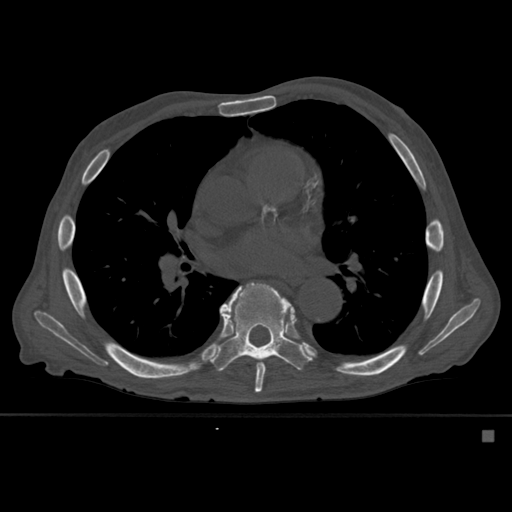
CT including the spine, one axial slice. Position 355 of 527 along the scan axis. Bone window (W 1800 / L 400 HU). 512 × 512 image matrix, field of view 373 × 373 mm. Male patient, age 78 years. From the clinical record (not read from this slice): primary cancer: prostate.
Outlined on this slice (semi-automatically segmented with operator editing):
- T7 vertebra: bounding box <223,284,294,393> (left, top, right, bottom; pixels)
- T8 vertebra: <210,283,310,371>